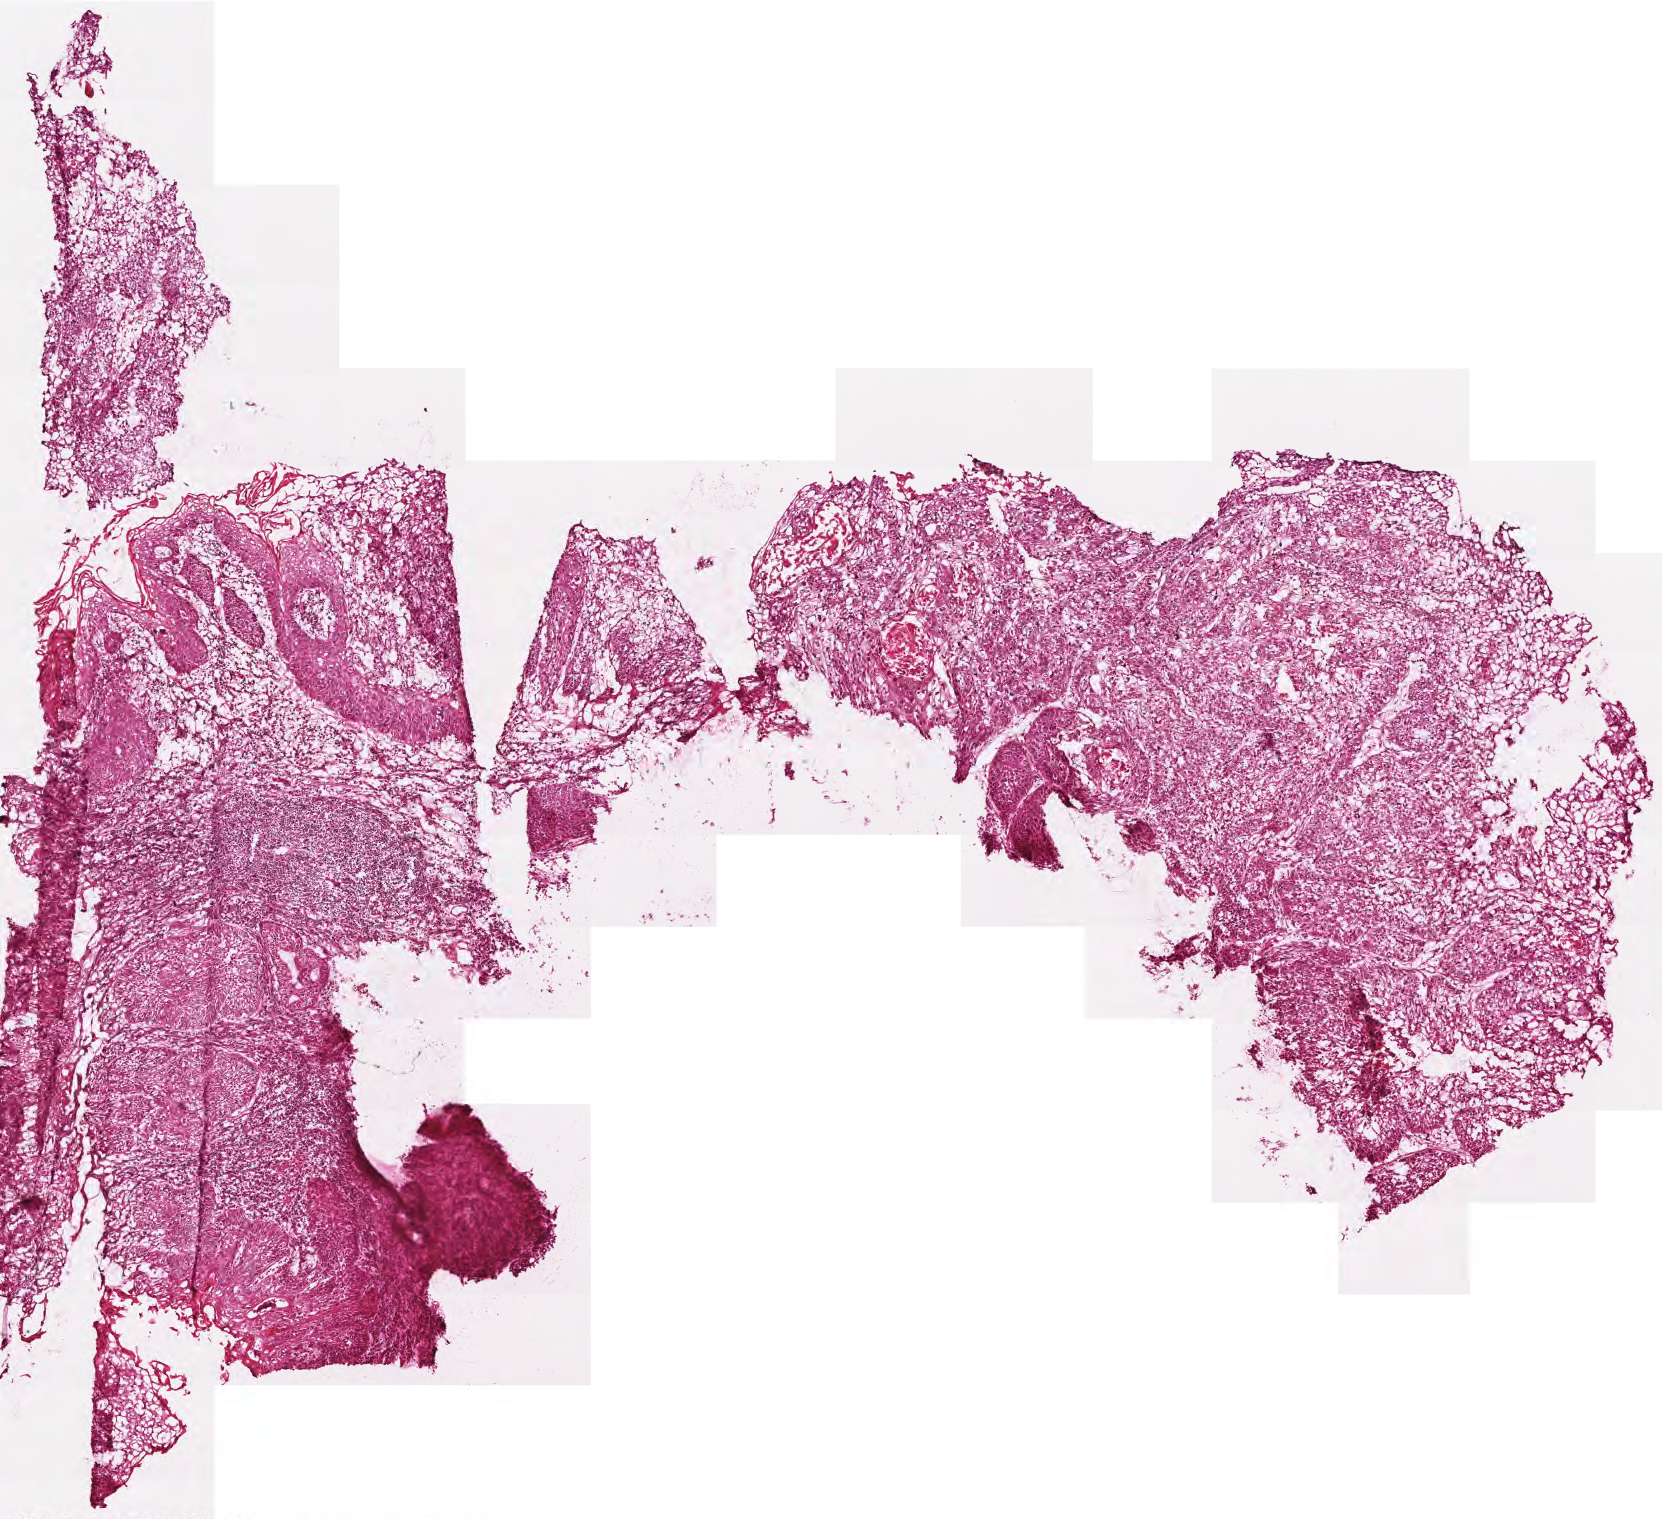
Whole-slide histology image, Hematoxylin and eosin (H&E) stained, a low-resolution overview of the entire scanned area, about 3.3 x 3.0 mm; frozen section from the top of the tissue portion; sample: primary tumour, head and neck. Female, age 67 years at initial diagnosis. Histologic grade: G2 (moderately differentiated). Composition of this section per pathologist review: tumour cells 85%, tumour nuclei 65%, normal cells 0%, stromal cells 15%, necrosis 0%.
Laterality: left. Diagnosis: Squamous cell carcinoma, NOS (larynx, NOS).